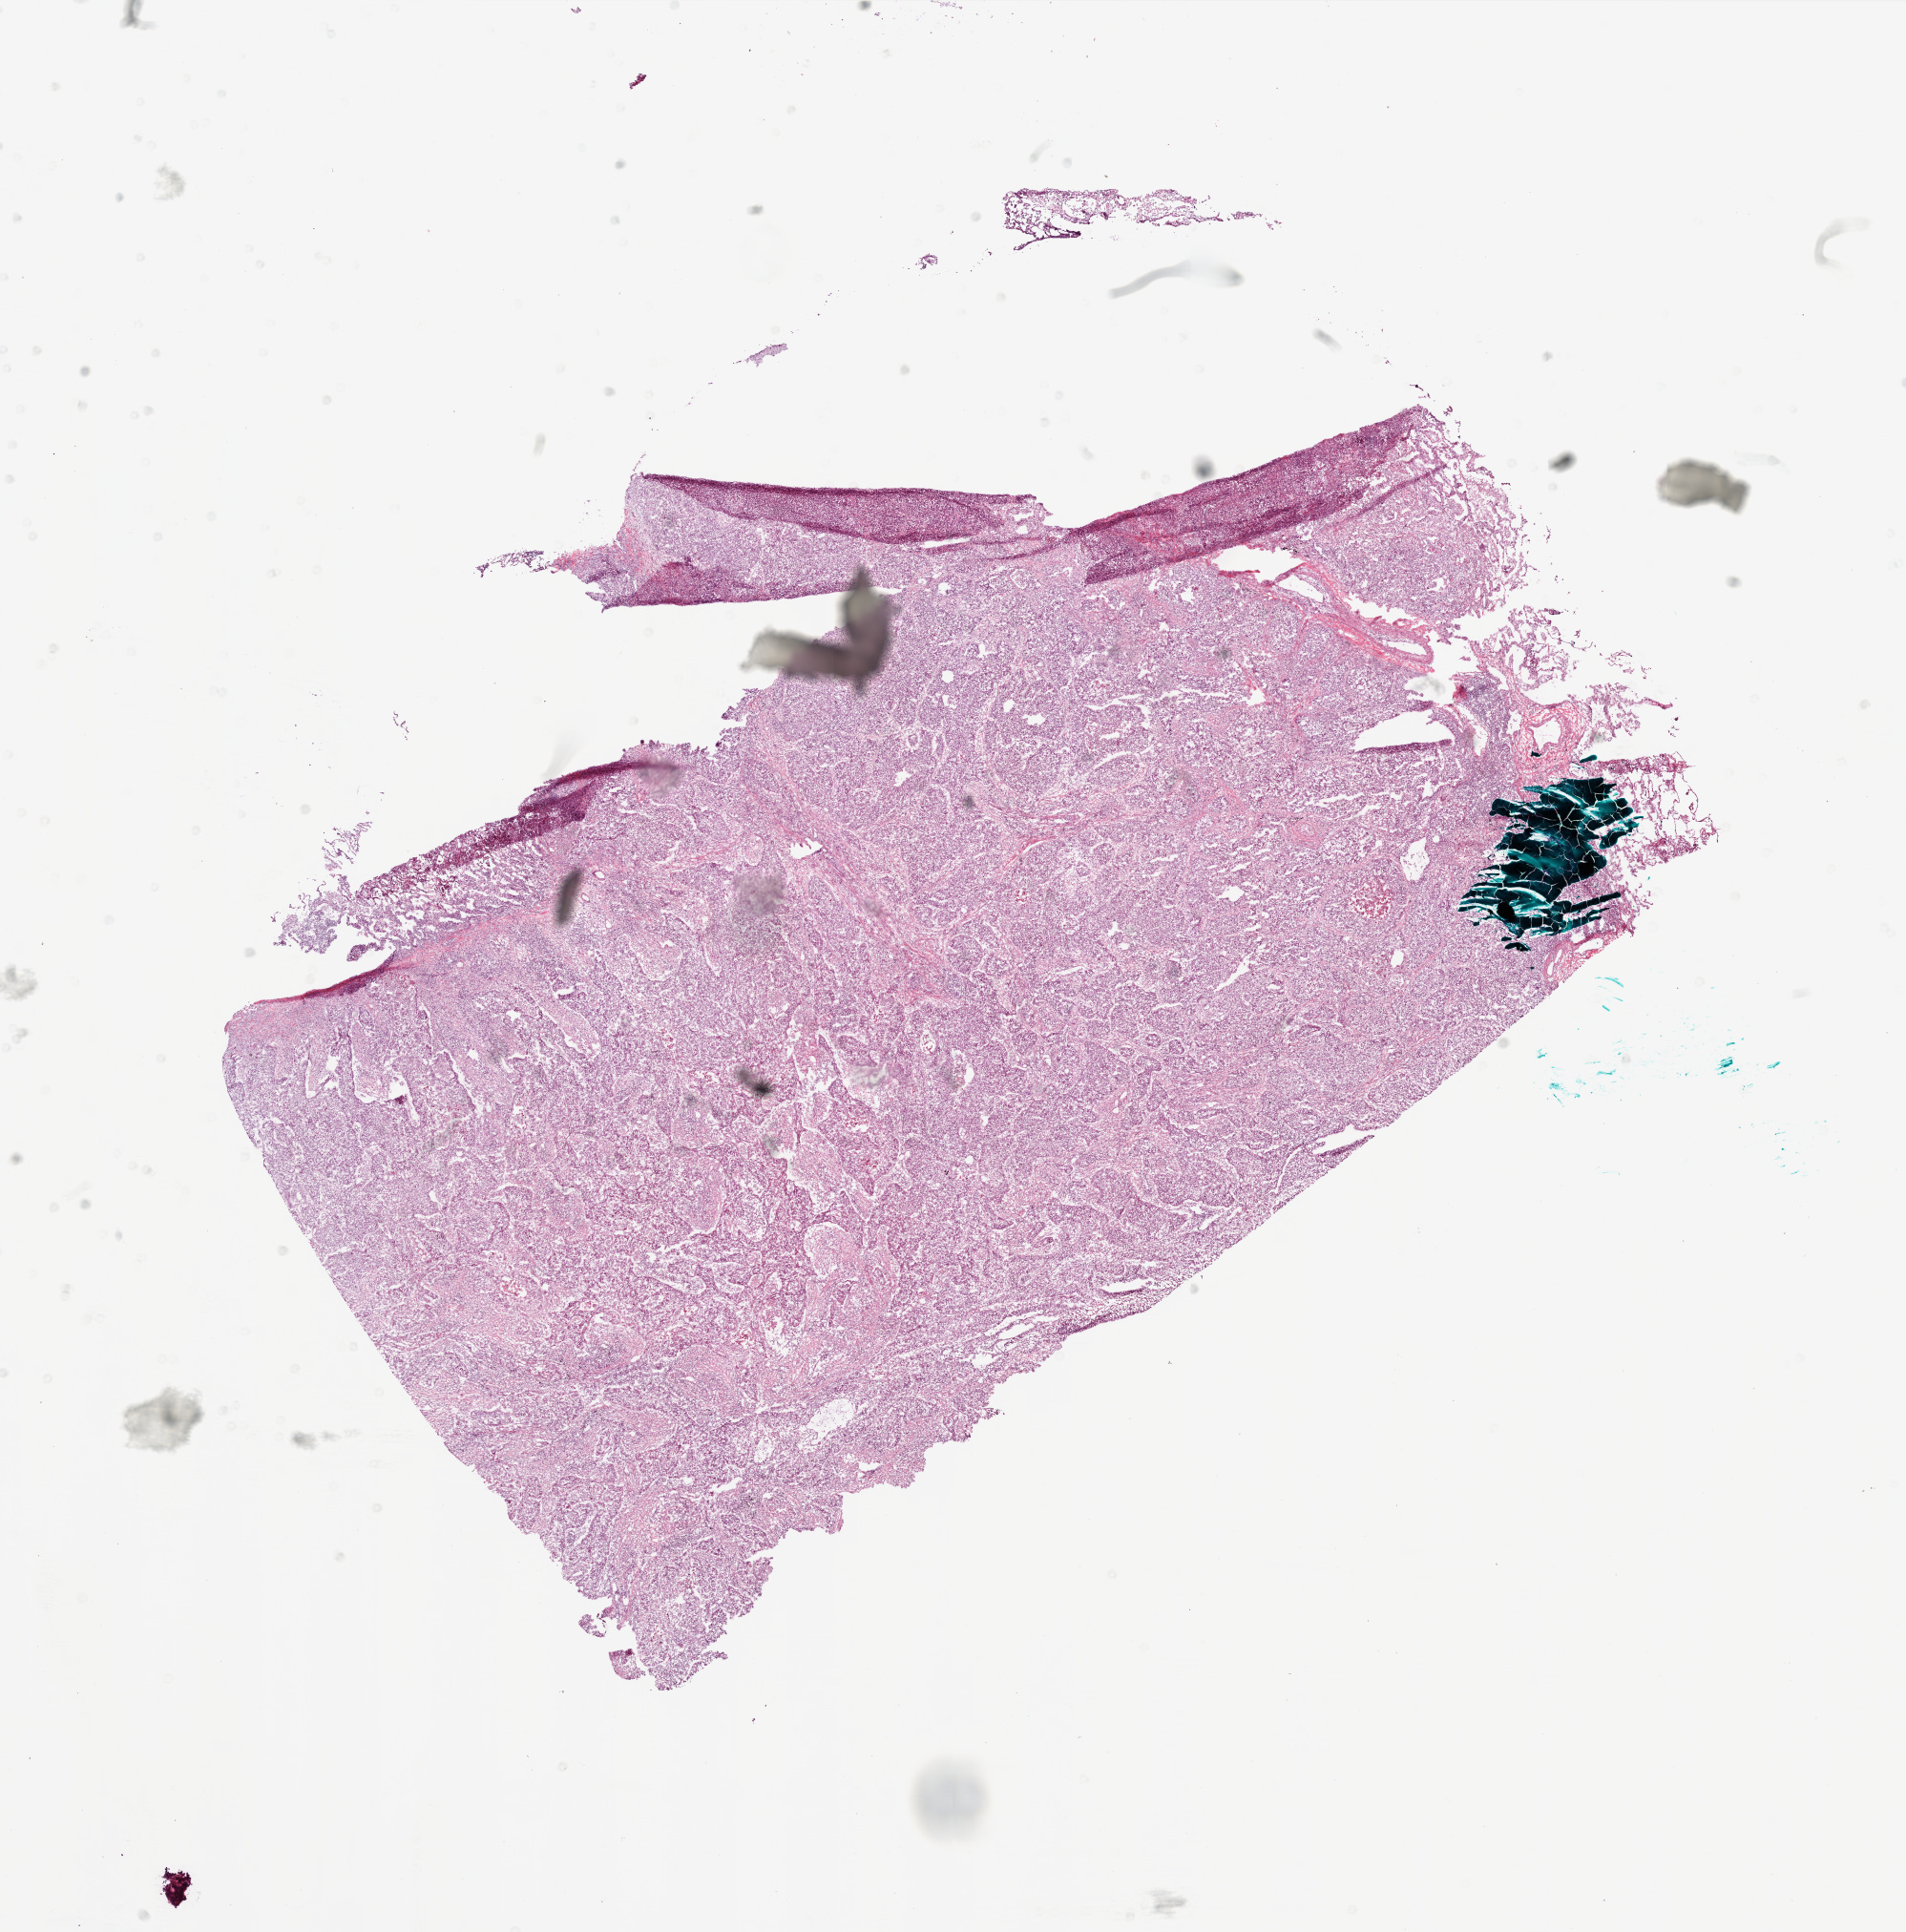
H&E whole-slide image — a low-resolution overview of the entire scanned area, about 16.0 x 16.2 mm (from a 20x scan). Frozen section from the bottom of the tissue portion. Primary tumour sample from the lung. Patient: male, age at initial diagnosis 71 years. Composition of this section per pathologist review: tumour nuclei 80%, necrosis 0%.
Diagnosis: Squamous cell carcinoma, NOS. AJCC pathologic stage: IIA.